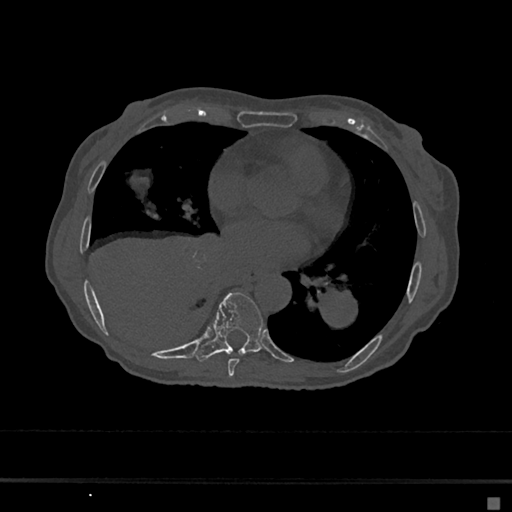
CT including the spine, one axial slice; slice 339 of 797 in the series (ordered by position); reconstruction kernel Br40s/3; 120 kVp; bone window (W 1800 / L 400 HU); 0.5 mm slice thickness; 512 × 512 image matrix, field of view 360 × 360 mm. Patient: female, 68 years. Case-level facts recorded for this patient, not image findings: primary cancer: renal.
Structures marked on this image (semi-automatically segmented with operator editing):
- T7 vertebra: bounding box [x1, y1, x2, y2] px = [228, 359, 239, 377]
- T8 vertebra: [196, 292, 263, 362]